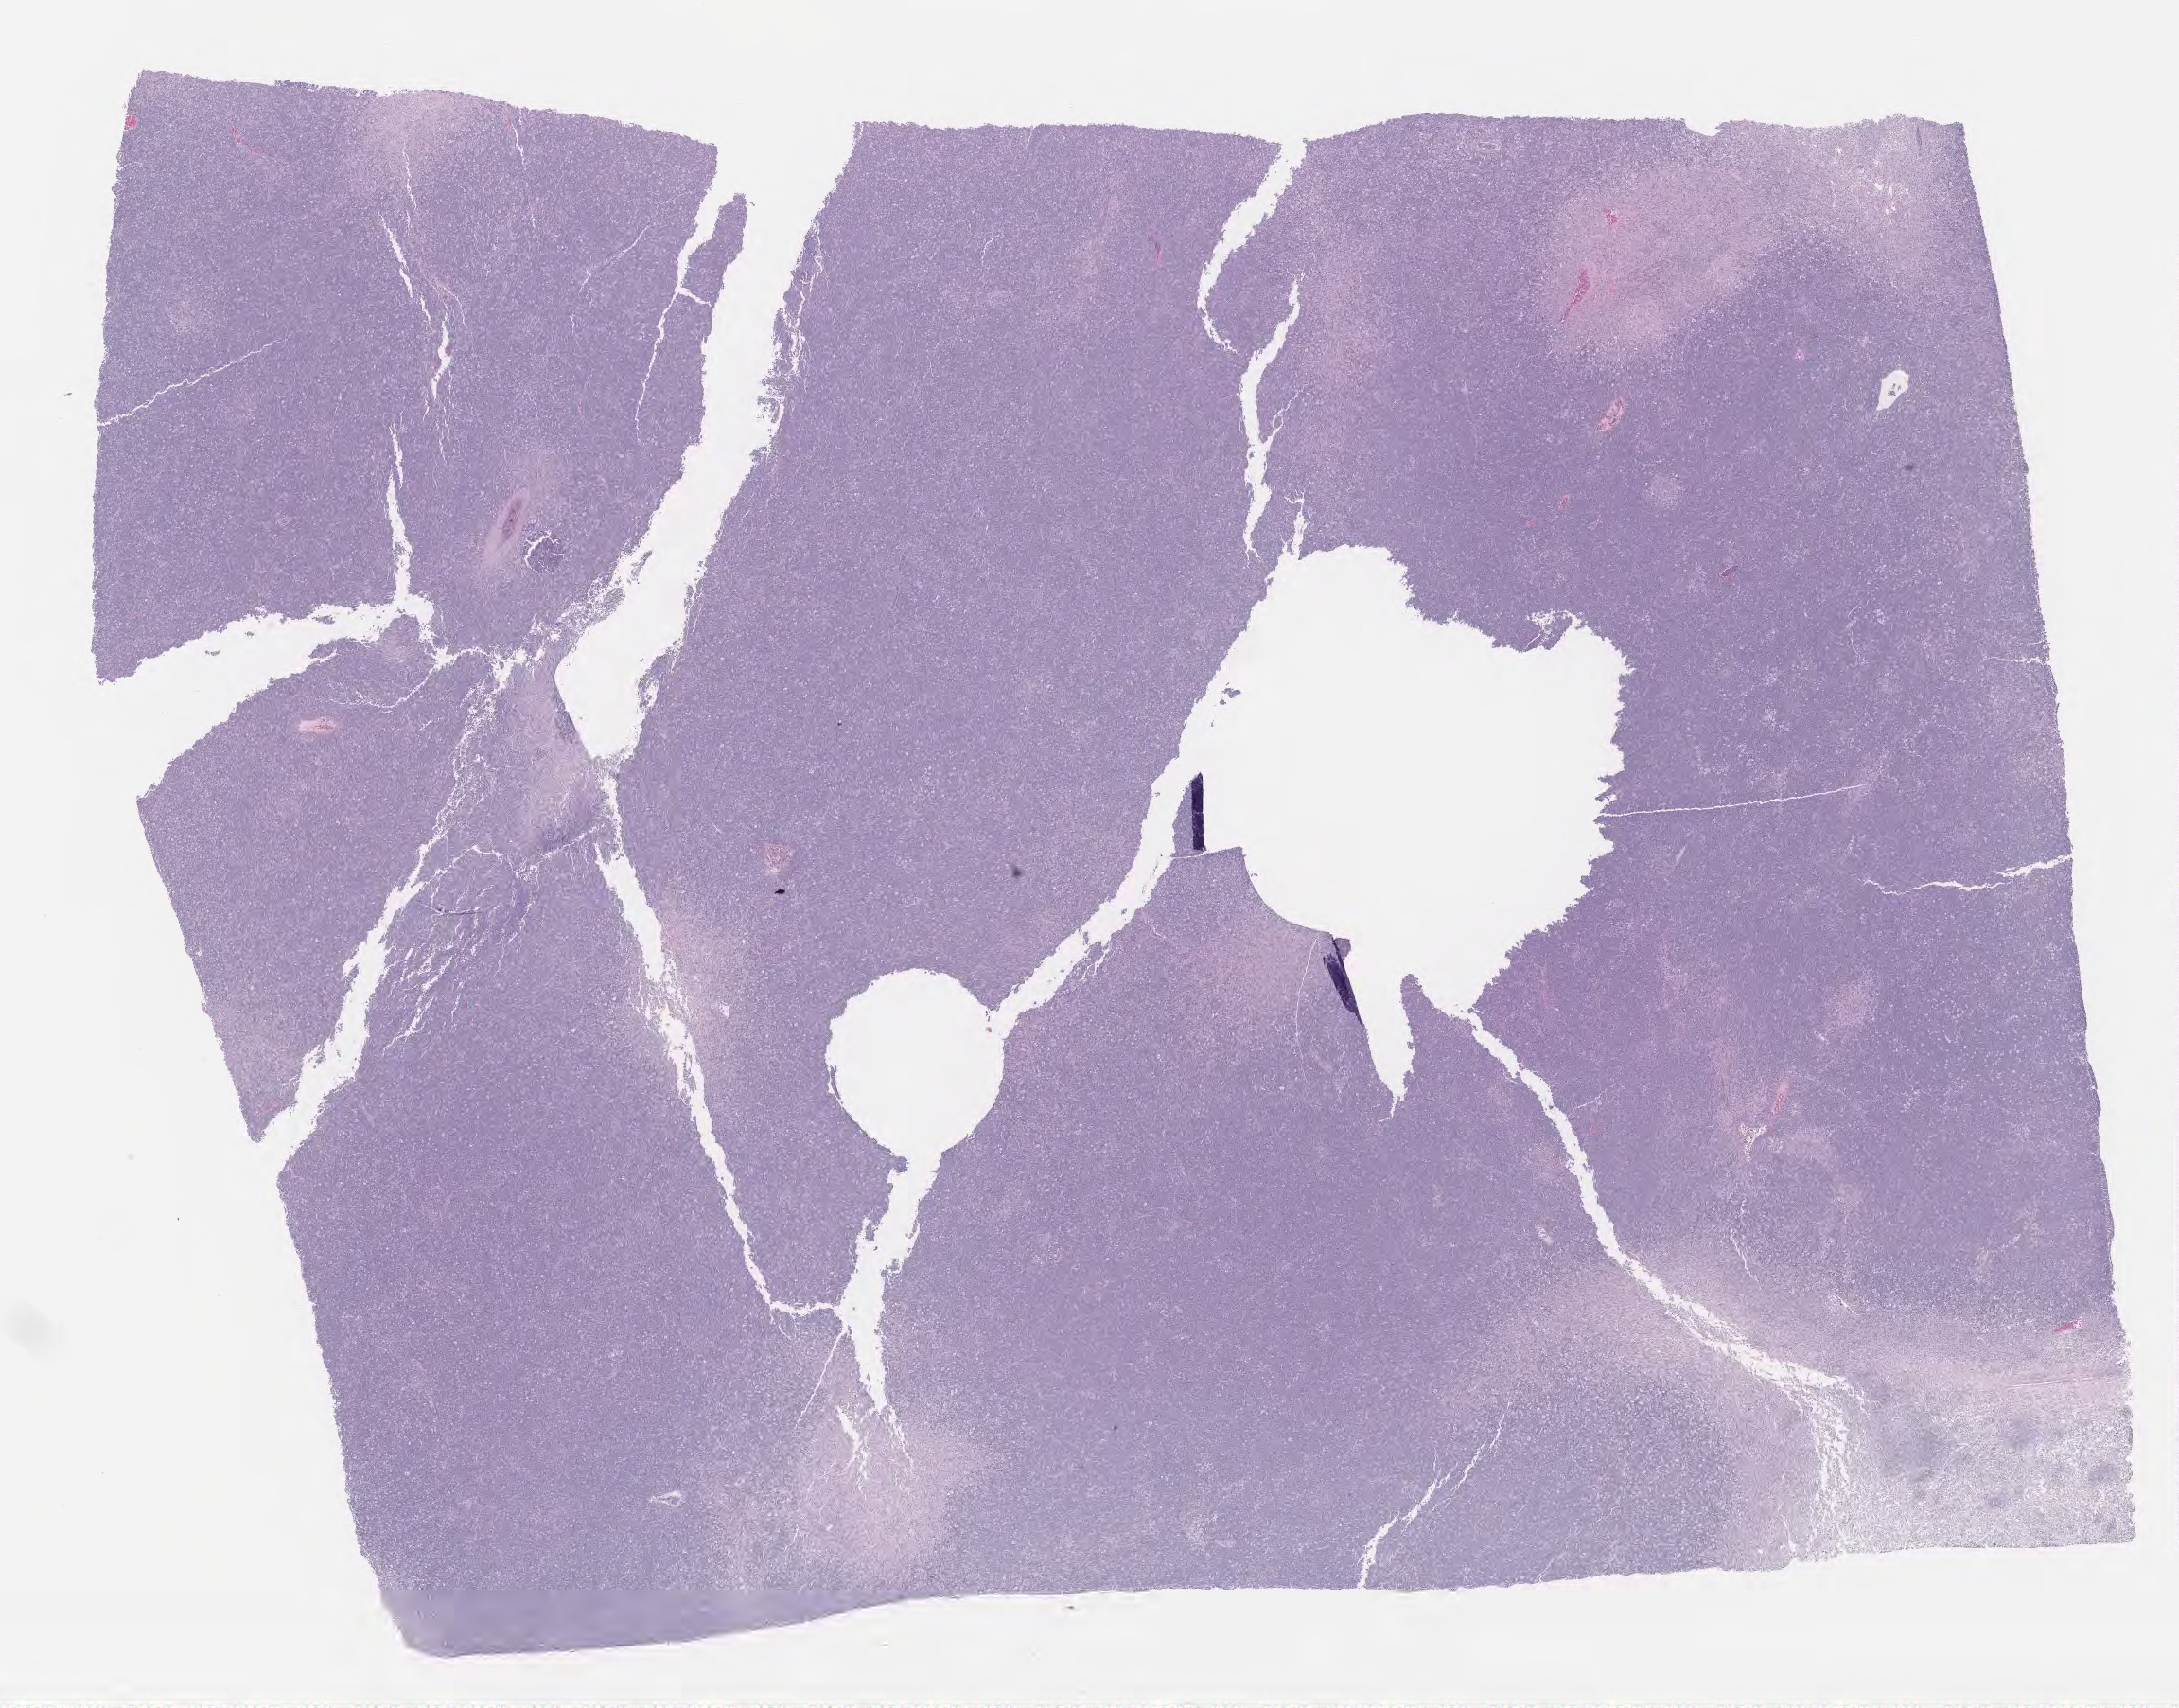
Whole-slide image, H&E stain, low-resolution overview of the scanned area, about 18.6 x 14.6 mm. Specimen: tumor tissue. Site: ovary. Patient female; aged 53.
• histologic diagnosis: Burkitt lymphoma, NOS